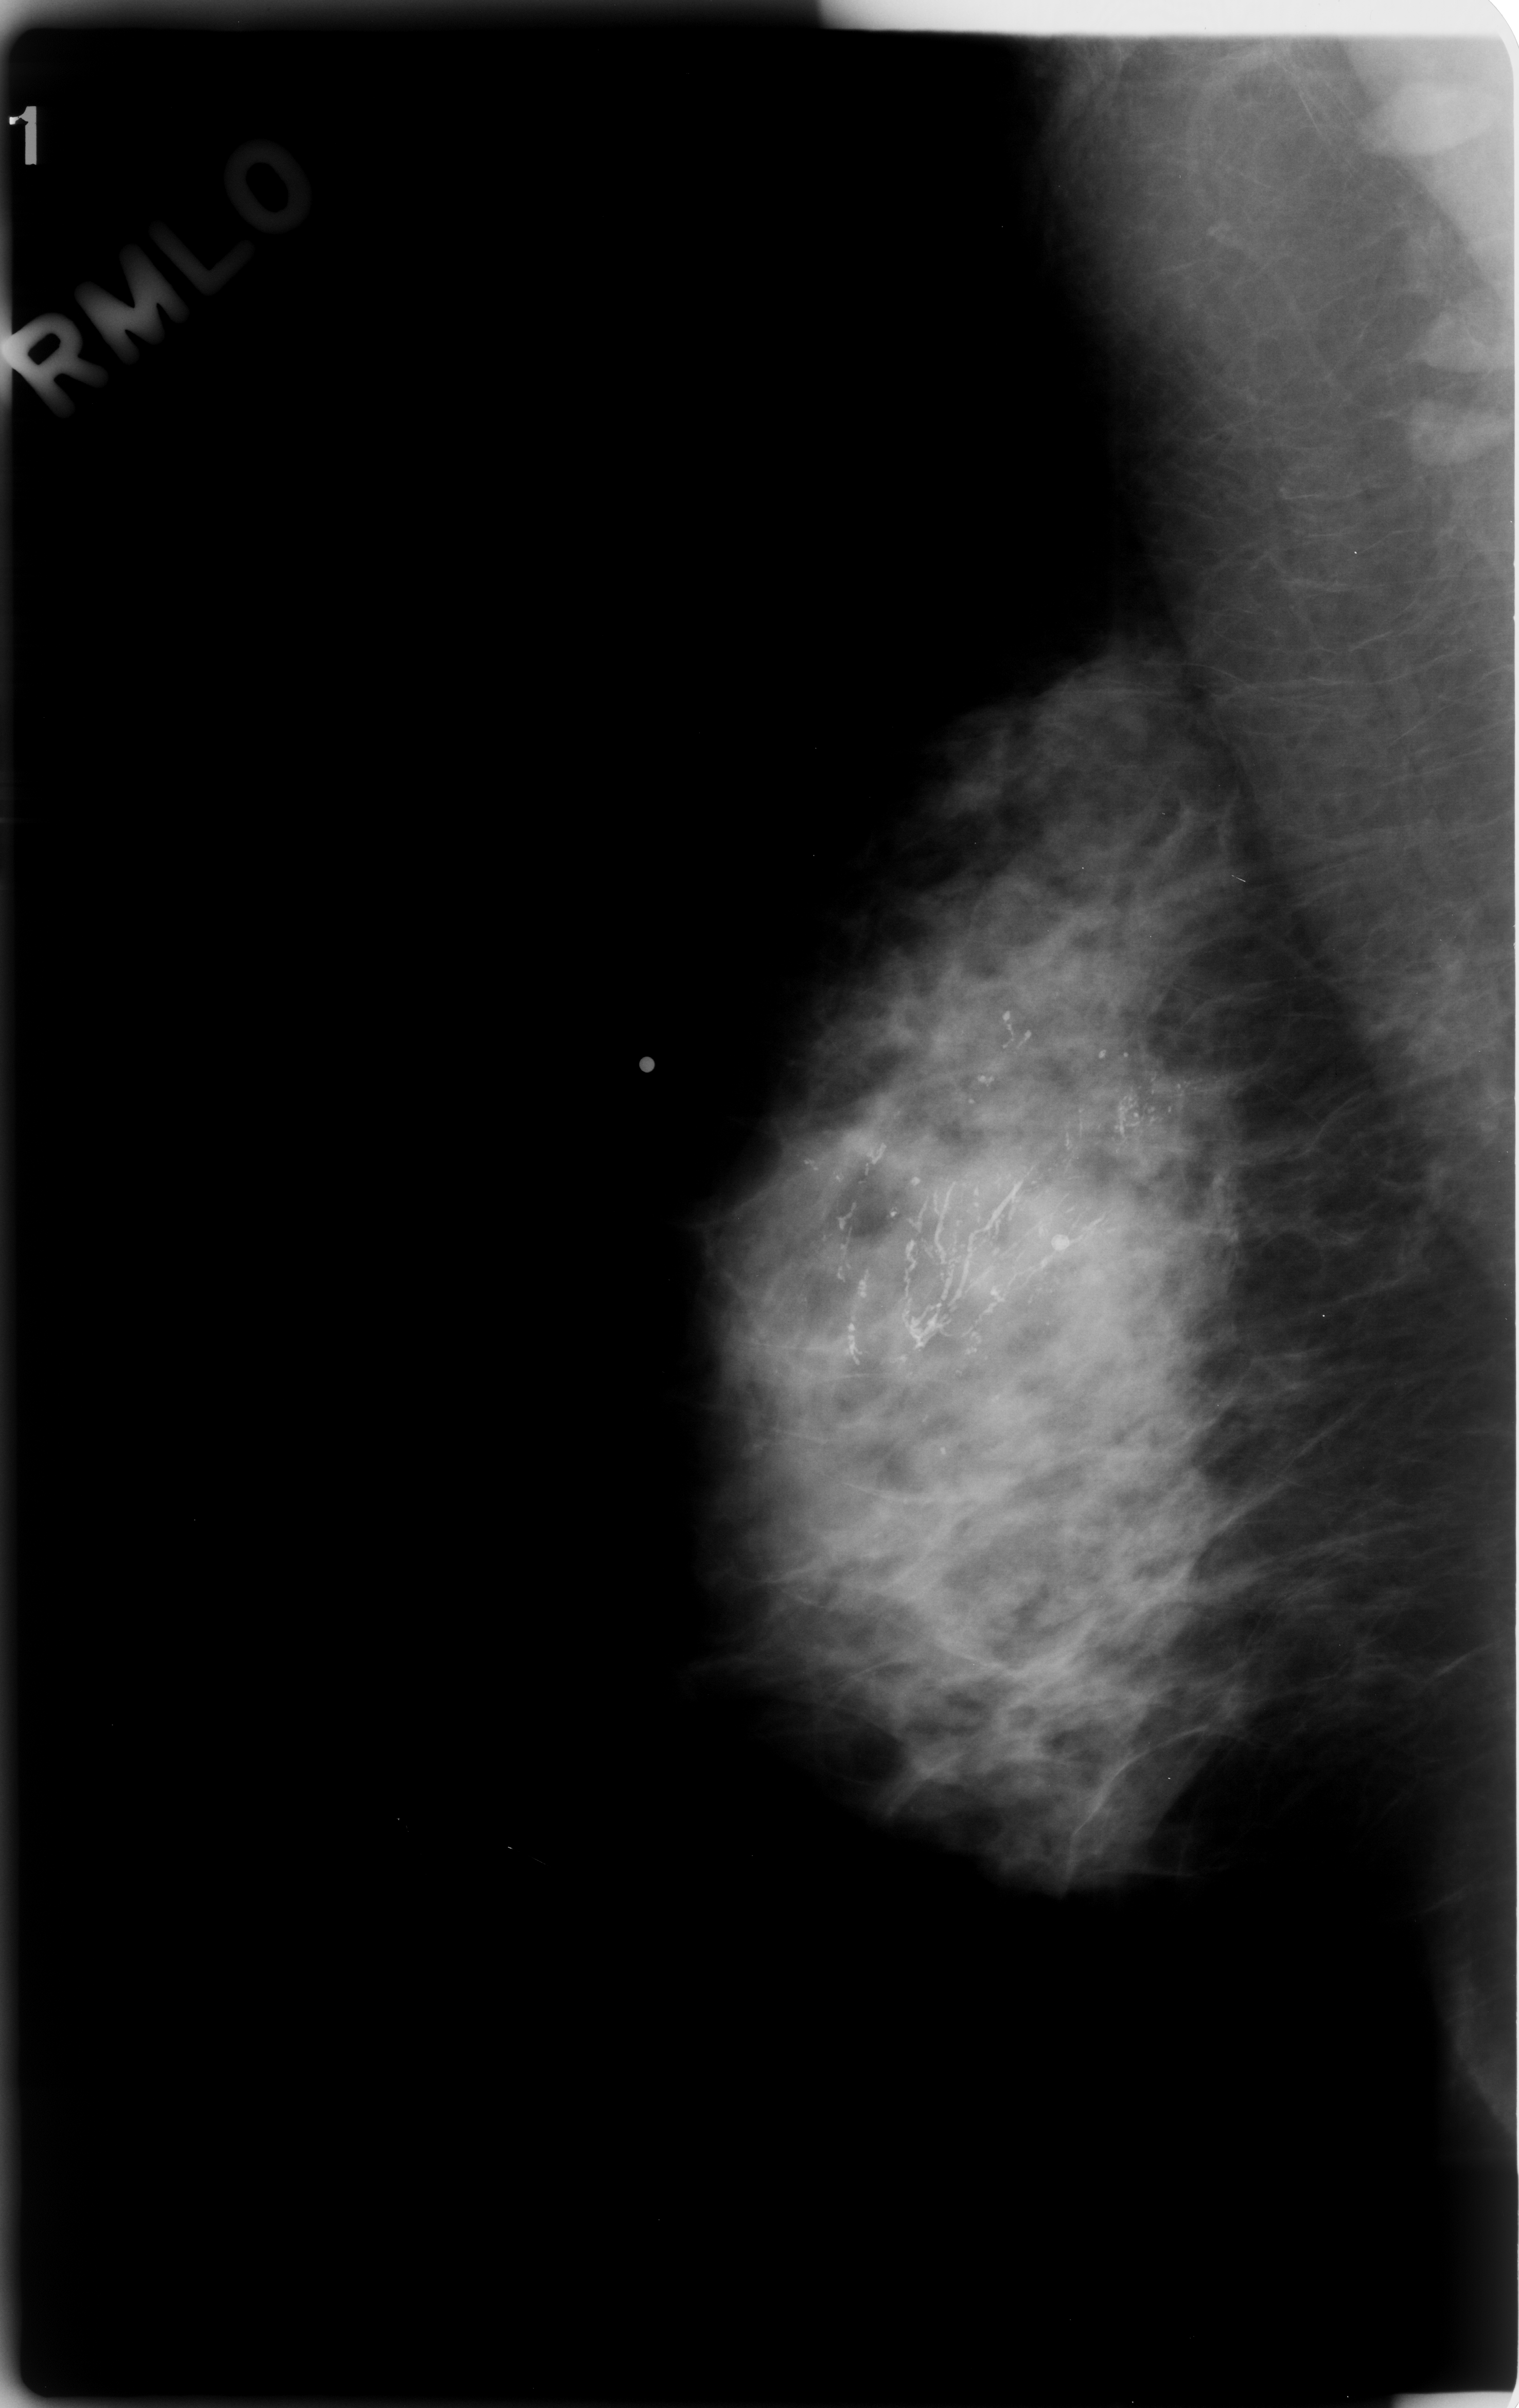
Mammogram (digitized film); right breast; mediolateral oblique (MLO) view; BI-RADS breast density category 3 (scale 1–4); 1519 × 2408 image matrix.
Marked abnormalities (boxes around the expert regions of interest):
- calcifications, morphology fine linear branching, distribution segmental; BI-RADS assessment category 5; pathology result (as recorded, not read from the image): malignant: bounding box (x1, y1, x2, y2) in pixels: (827, 1008, 1314, 1516)